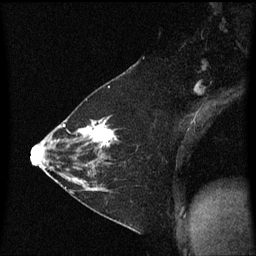
Breast MRI (dynamic contrast-enhanced), one sagittal slice; slice 37 of 60 in the series (ordered by position); dynamic contrast-enhanced series, image 2 of 3 at this slice position (ordered by acquisition); 1.5 T; TE 4.2 ms, TR 8.4 ms; 2 mm slice thickness; 256 × 256 image matrix. Patient: female, 36 years. From the clinical record (not read from this slice): setting: breast cancer imaged before/during neoadjuvant chemotherapy; receptor status: HR-positive, HER2-negative.
Annotated regions visible in this slice (semi-automatically segmented with operator editing):
- analysis volume of interest (the breast-tissue region the enhancement analysis was run in; not a lesion): bounding box (x1, y1, x2, y2) in pixels: (72, 116, 121, 187)
- tumour enhancement mask (voxels above the 70 % enhancement threshold inside the analysis volume of interest): (76, 120, 117, 183)